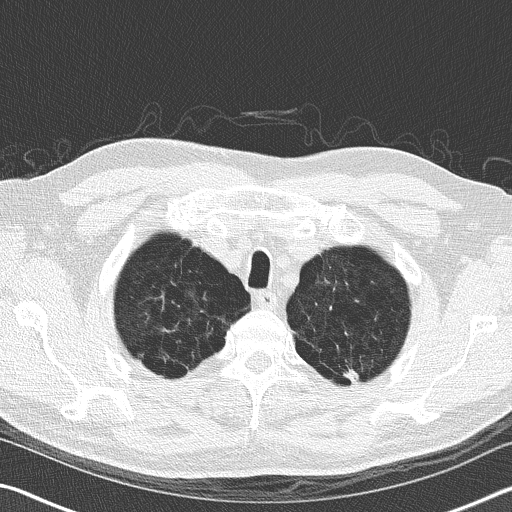
Low-dose screening chest CT, axial slice. Baseline screening round. Lung window (W 1500 / L -600 HU). 2 mm slice thickness. Lung (sharp) reconstruction kernel (B50f). 120 kVp. Male participant, aged 62 years at enrolment.
Expert reader's lesion annotation, box from (x=332, y=353) to (x=373, y=393) px. The exam's reader record, not a measurement of the box and not confirmed to be the same lesion: non-calcified nodule or mass ≥4 mm, left upper lobe, 10 × 10 mm. Official screen result: positive, change unspecified: nodule(s) >= 4 mm or enlarging nodule(s), mass(es), or other non-specific abnormalities suspicious for lung cancer. Participant outcome: lung cancer diagnosed 561 days after this screen (after the second annual screen) — adenocarcinoma, NOS, left upper lobe, moderately differentiated (G2), stage IA (AJCC 6th edition), 10 mm at pathology.